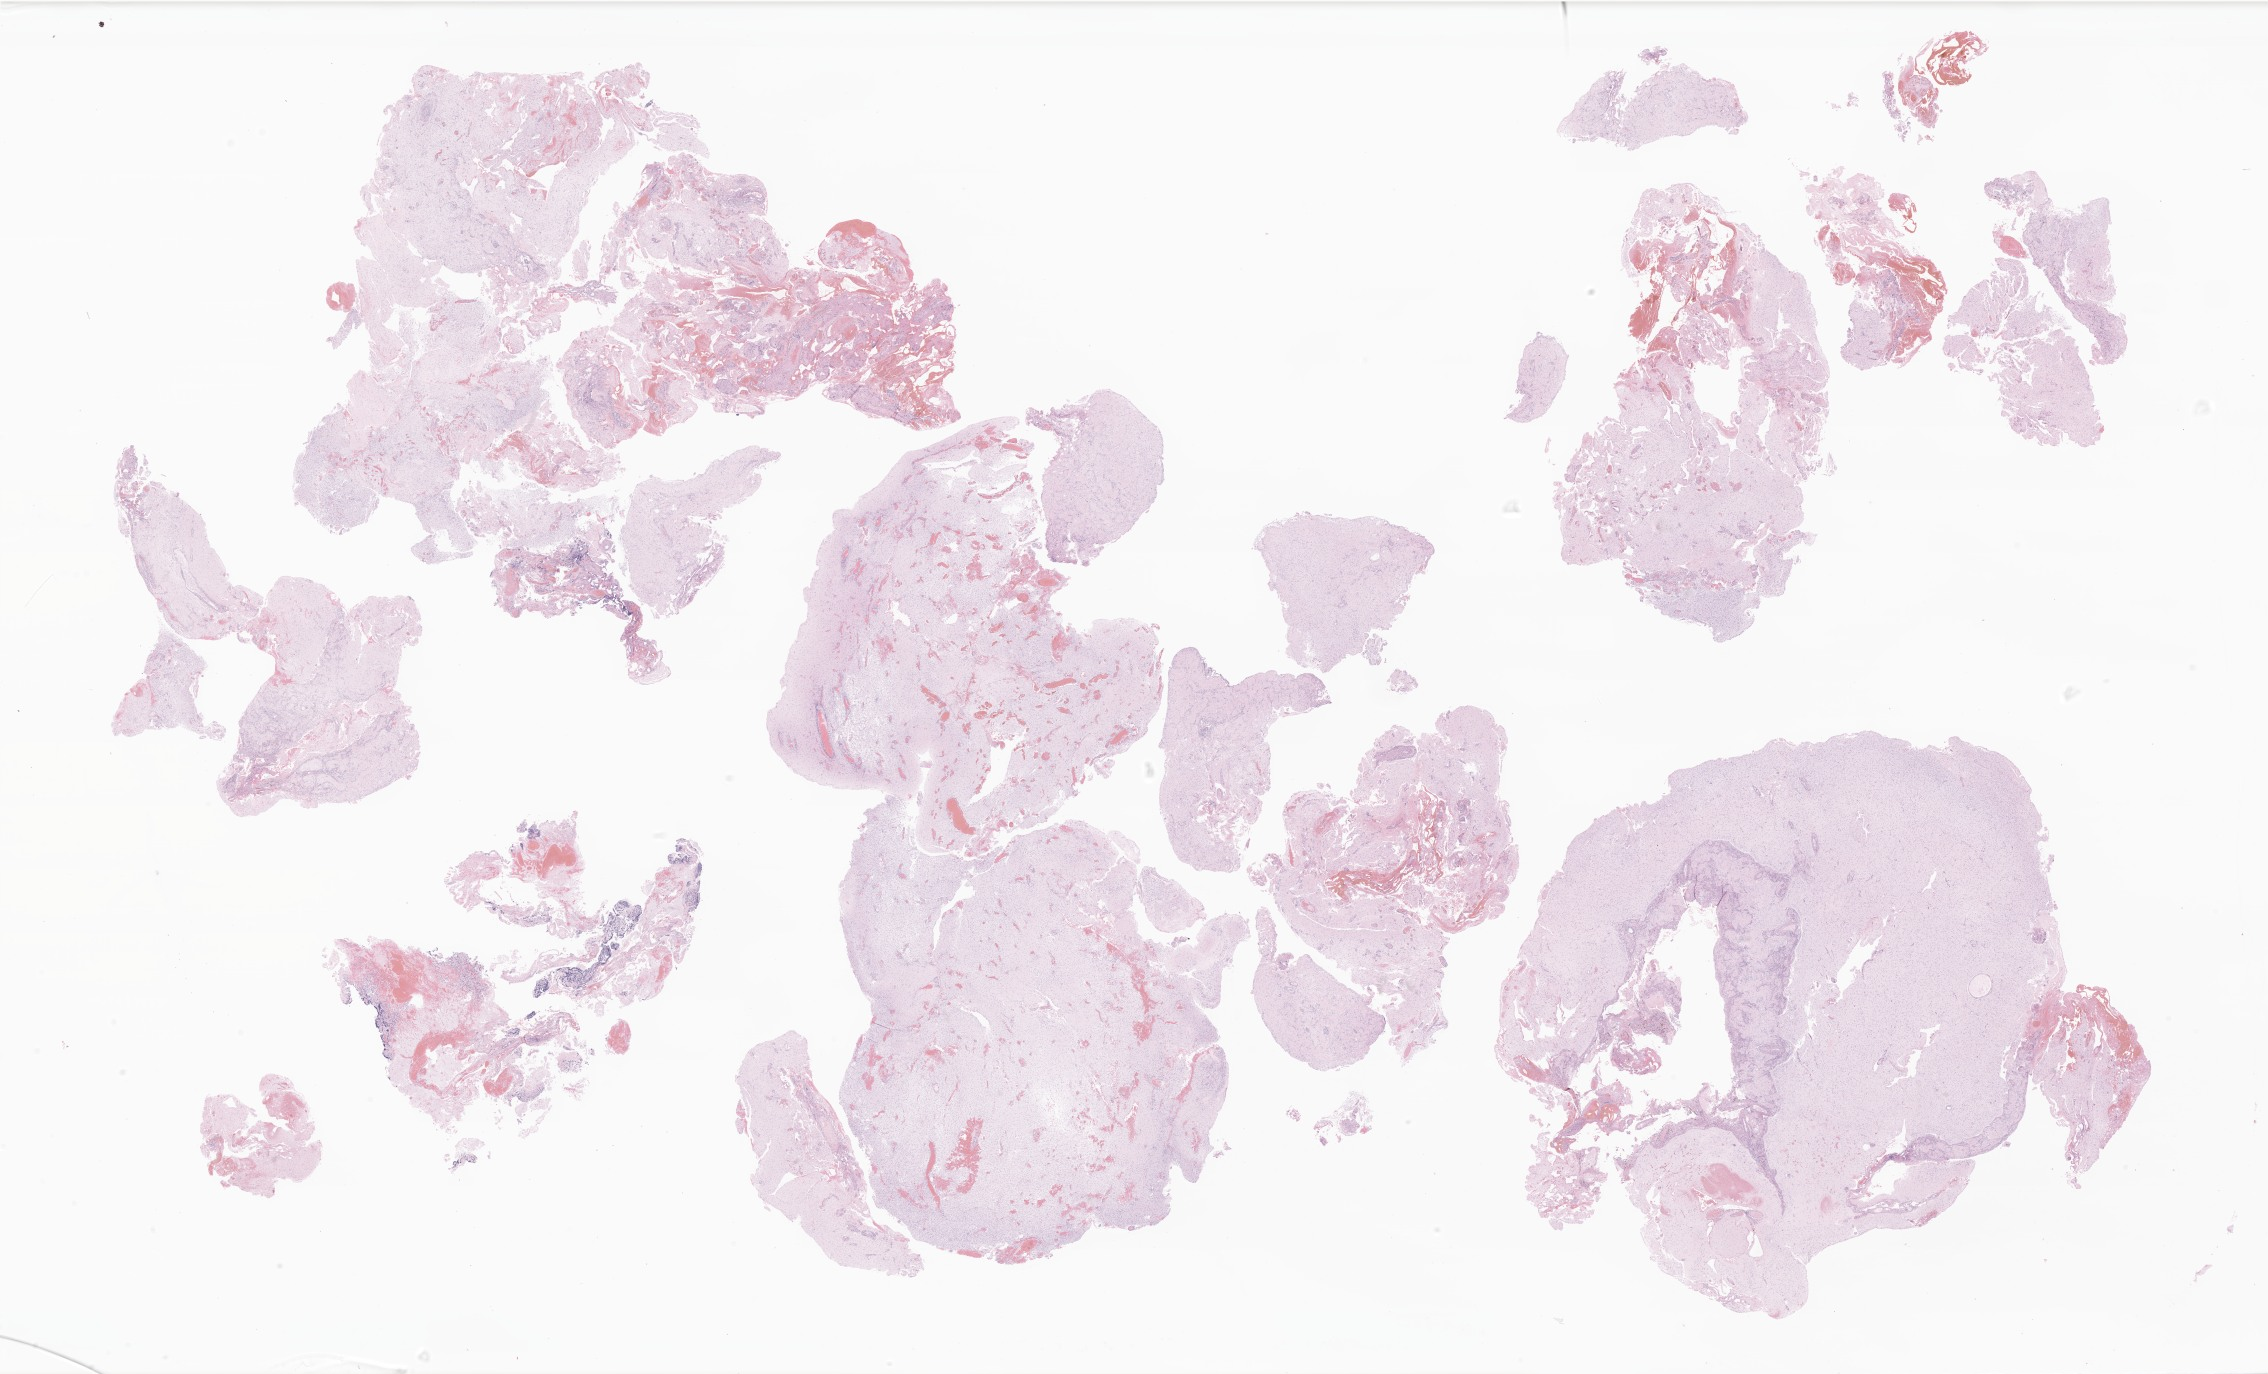
Whole-slide image, haematoxylin and eosin stain of tumor tissue from the brain — whole scanned area (about 38.3 x 23.2 mm) shown as a low-resolution overview, formalin-fixed, paraffin-embedded (FFPE) tissue. Patient female; age 157 months (13 years 1 month).
* diagnosis: Pilocytic astrocytoma